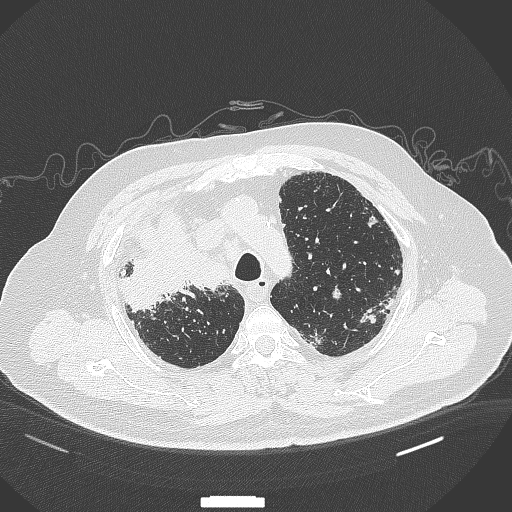
Chest CT, one axial slice. Position 282 of 384 along the scan axis. Lung window (W 1500 / L -600 HU). 512 × 512 image matrix. Male patient, age 69 years. Case-level facts recorded for this patient, not image findings: clinical TNM (as recorded): T4 N3 M1.
Annotated regions visible in this slice (rectangle marked by the reading radiologist):
- lung tumour (recorded histology: adenocarcinoma): box from (x=117, y=215) to (x=230, y=309) px